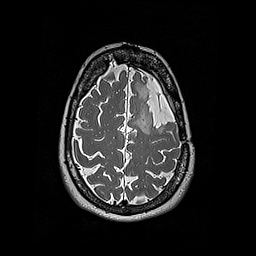
Brain MRI from a brain-tumour surgery series, one axial slice. Slice 140 of 192 in the series (ordered by position). 1 mm slice thickness. 256 × 256 image matrix. From the clinical record (not read from this slice): histopathology: Oligodendroglioma; WHO grade: 2.
Structures marked on this image (manually delineated by an expert):
- tumour: bounding box <144,113,154,134> (left, top, right, bottom; pixels)